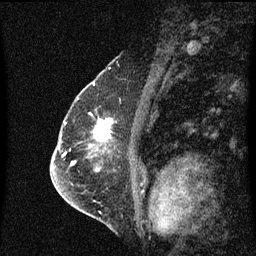
Breast MRI (dynamic contrast-enhanced), one sagittal slice; slice 41 of 60 in the series (ordered by position); dynamic contrast-enhanced series, image 2 of 3 at this slice position (ordered by acquisition); 1.5 T; TE 4.2 ms, TR 8.4 ms; 2 mm slice thickness; 256 × 256 image matrix, field of view 200 × 200 mm. Female patient, age 57 years. Case-level facts recorded for this patient, not image findings: setting: breast cancer imaged before/during neoadjuvant chemotherapy; receptor status: HR-positive, HER2-negative.
Annotated regions visible in this slice (semi-automatic segmentation, software-assisted and operator-edited):
- analysis volume of interest (the breast-tissue region the enhancement analysis was run in; not a lesion): box from (x=85, y=110) to (x=114, y=145) px
- tumour enhancement mask (voxels above the 70 % enhancement threshold inside the analysis volume of interest): (x=96, y=120)–(x=114, y=141)